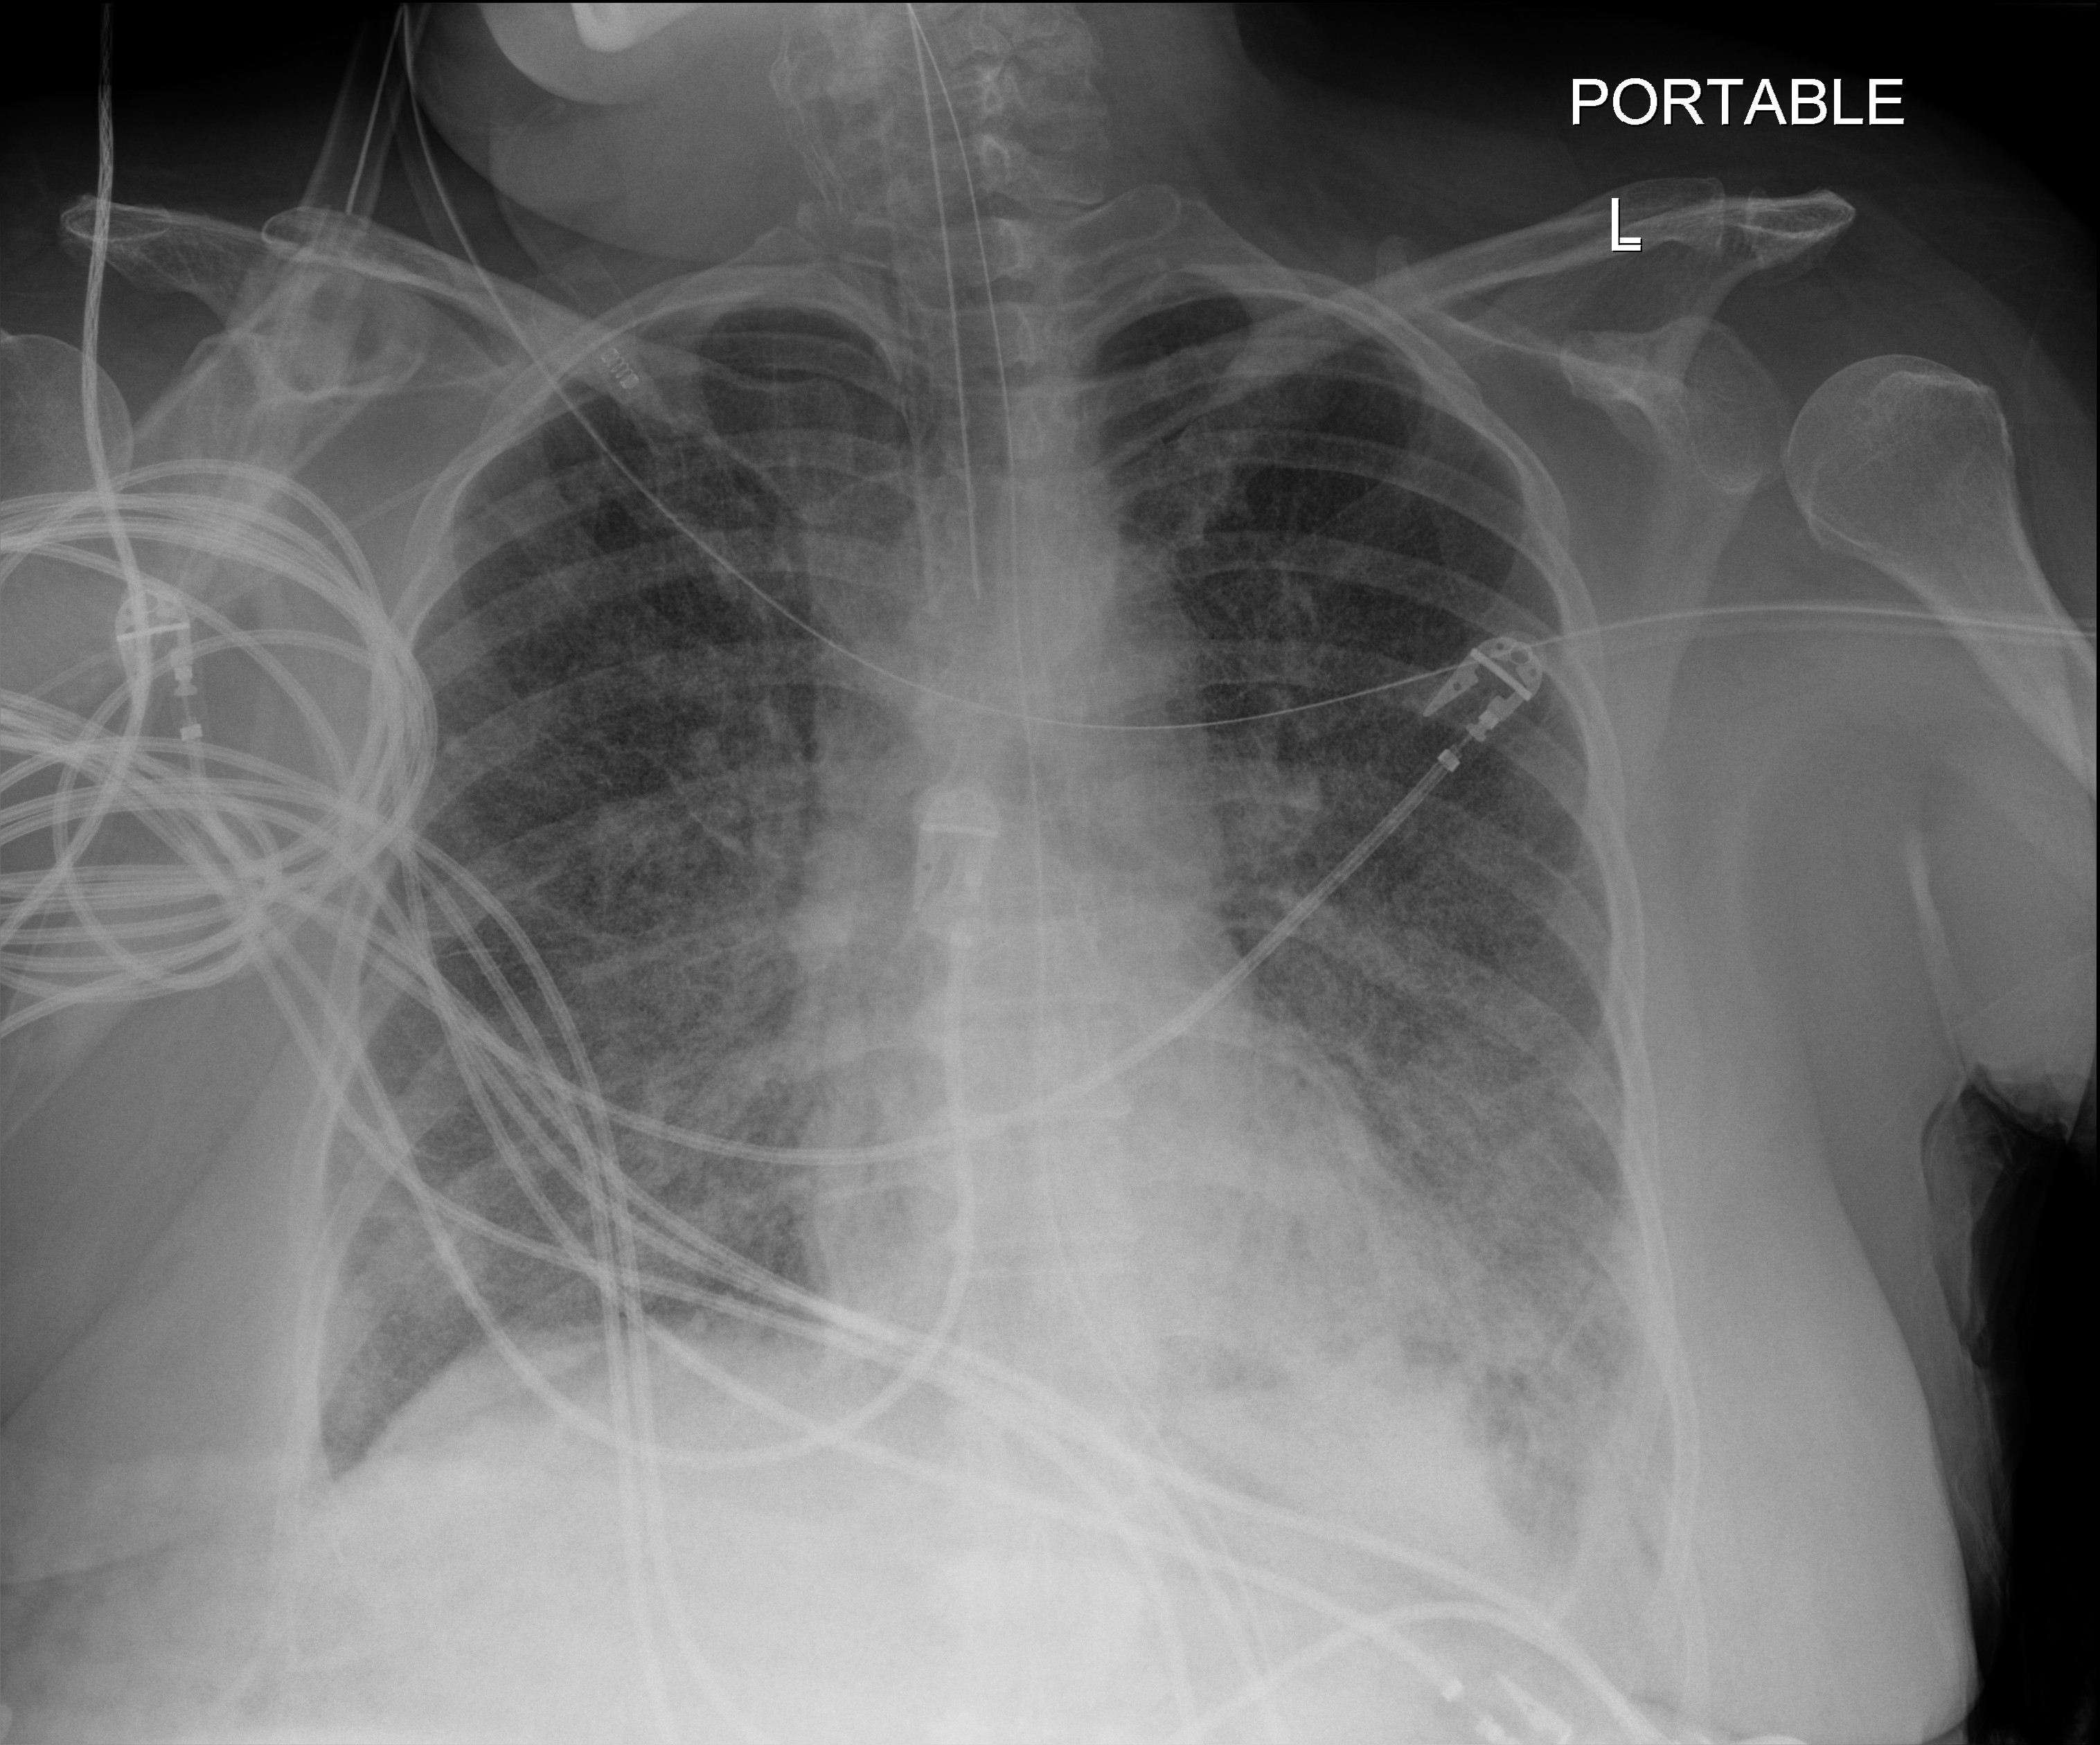
Chest X-ray (portable); anteroposterior (AP) projection. Patient hospitalised with COVID-19; female, aged 60–74 years.
Admission-level facts for this patient (not findings on this image; timing relative to this image not recorded): admitted to intensive care during this hospital stay: yes; diabetes (admission record): no.